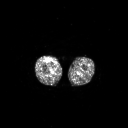
FDG PET of an extremity soft-tissue mass (from a PET/CT study), one axial slice. Slice 235 of 311 in the series (ordered by position). 128 × 128 image matrix. Patient: male, 56 years. From the clinical record (not read from this slice): histological type: pleiomorphic leiomyosarcoma; grade: intermediate; site of the primary tumour: right thigh.
Structures marked on this image (expert contour drawn on MRI and transferred to this co-registered scan by the dataset authors):
- gross tumour volume including surrounding oedema: box from (x=46, y=58) to (x=51, y=62) px